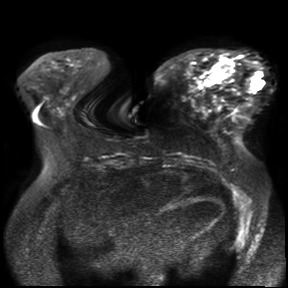
Breast MRI, one axial slice. Position 11 of 30 along the scan axis. Diffusion-weighted series; image 2 of 4 stored at this slice position (different b-values; order by instance number). 3 T. 288 × 288 image matrix, field of view 360 × 360 mm. Female patient.
Outlined on this slice (expert manual segmentation):
- tumour on diffusion-weighted imaging: bounding box [x1, y1, x2, y2] px = [208, 58, 230, 81]